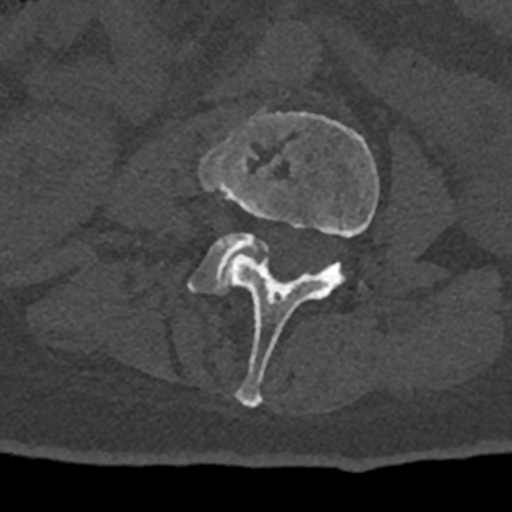
CT including the spine, one axial slice. Slice 306 of 797 in the series (ordered by position). Reconstruction kernel Br40s/3. 120 kVp. Bone window (W 1800 / L 400 HU). 0.5 mm slice thickness. 512 × 512 image matrix. Male patient, age 74 years. From the clinical record (not read from this slice): primary cancer: renal; vertebrae with lytic lesions (as recorded): T10, L1, L2, L3, L4, L5.
Structures marked on this image (semi-automatically segmented with operator editing):
- L3 vertebra: box from (x=199, y=110) to (x=379, y=408) px
- L4 vertebra: (x=188, y=232)–(x=268, y=295)